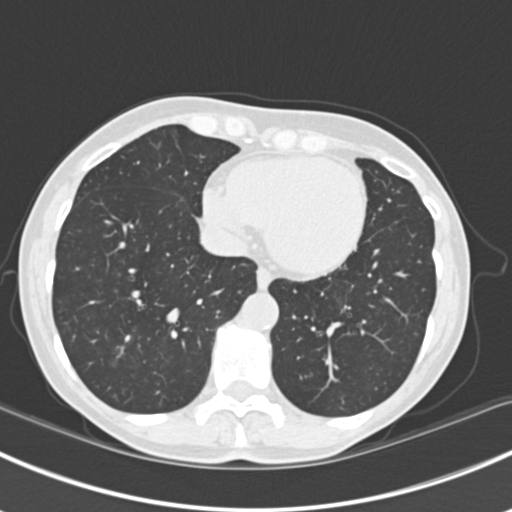
Chest CT (low-dose screening protocol), one axial image. Baseline screening round. Lung window (W 1500 / L -600 HU). 2 mm slice thickness. 512 × 512 image matrix. Female, age 63 years at enrolment. Current smoker at enrolment.
• Lesion marked by an expert reader, bounding box [x1, y1, x2, y2] px = [95, 332, 144, 373].
• The screening reader recorded 10 non-calcified nodules or masses ≥4 mm on this exam (right lower lobe, right lower lobe, left lower lobe, left lower lobe, right middle lobe, right lower lobe, left lower lobe, left upper lobe, right upper lobe, left upper lobe); which of them this box marks is not recorded.
• Official screen result: positive, change unspecified: nodule(s) >= 4 mm or enlarging nodule(s), mass(es), or other non-specific abnormalities suspicious for lung cancer.
• Later outcome: lung cancer diagnosed 751 days after this screen — bronchiolo-alveolar adenocarcinoma, NOS, right upper lobe, right middle lobe, right lower lobe, left upper lobe, left lower lobe, moderately differentiated (G2), stage IV (AJCC 6th edition).